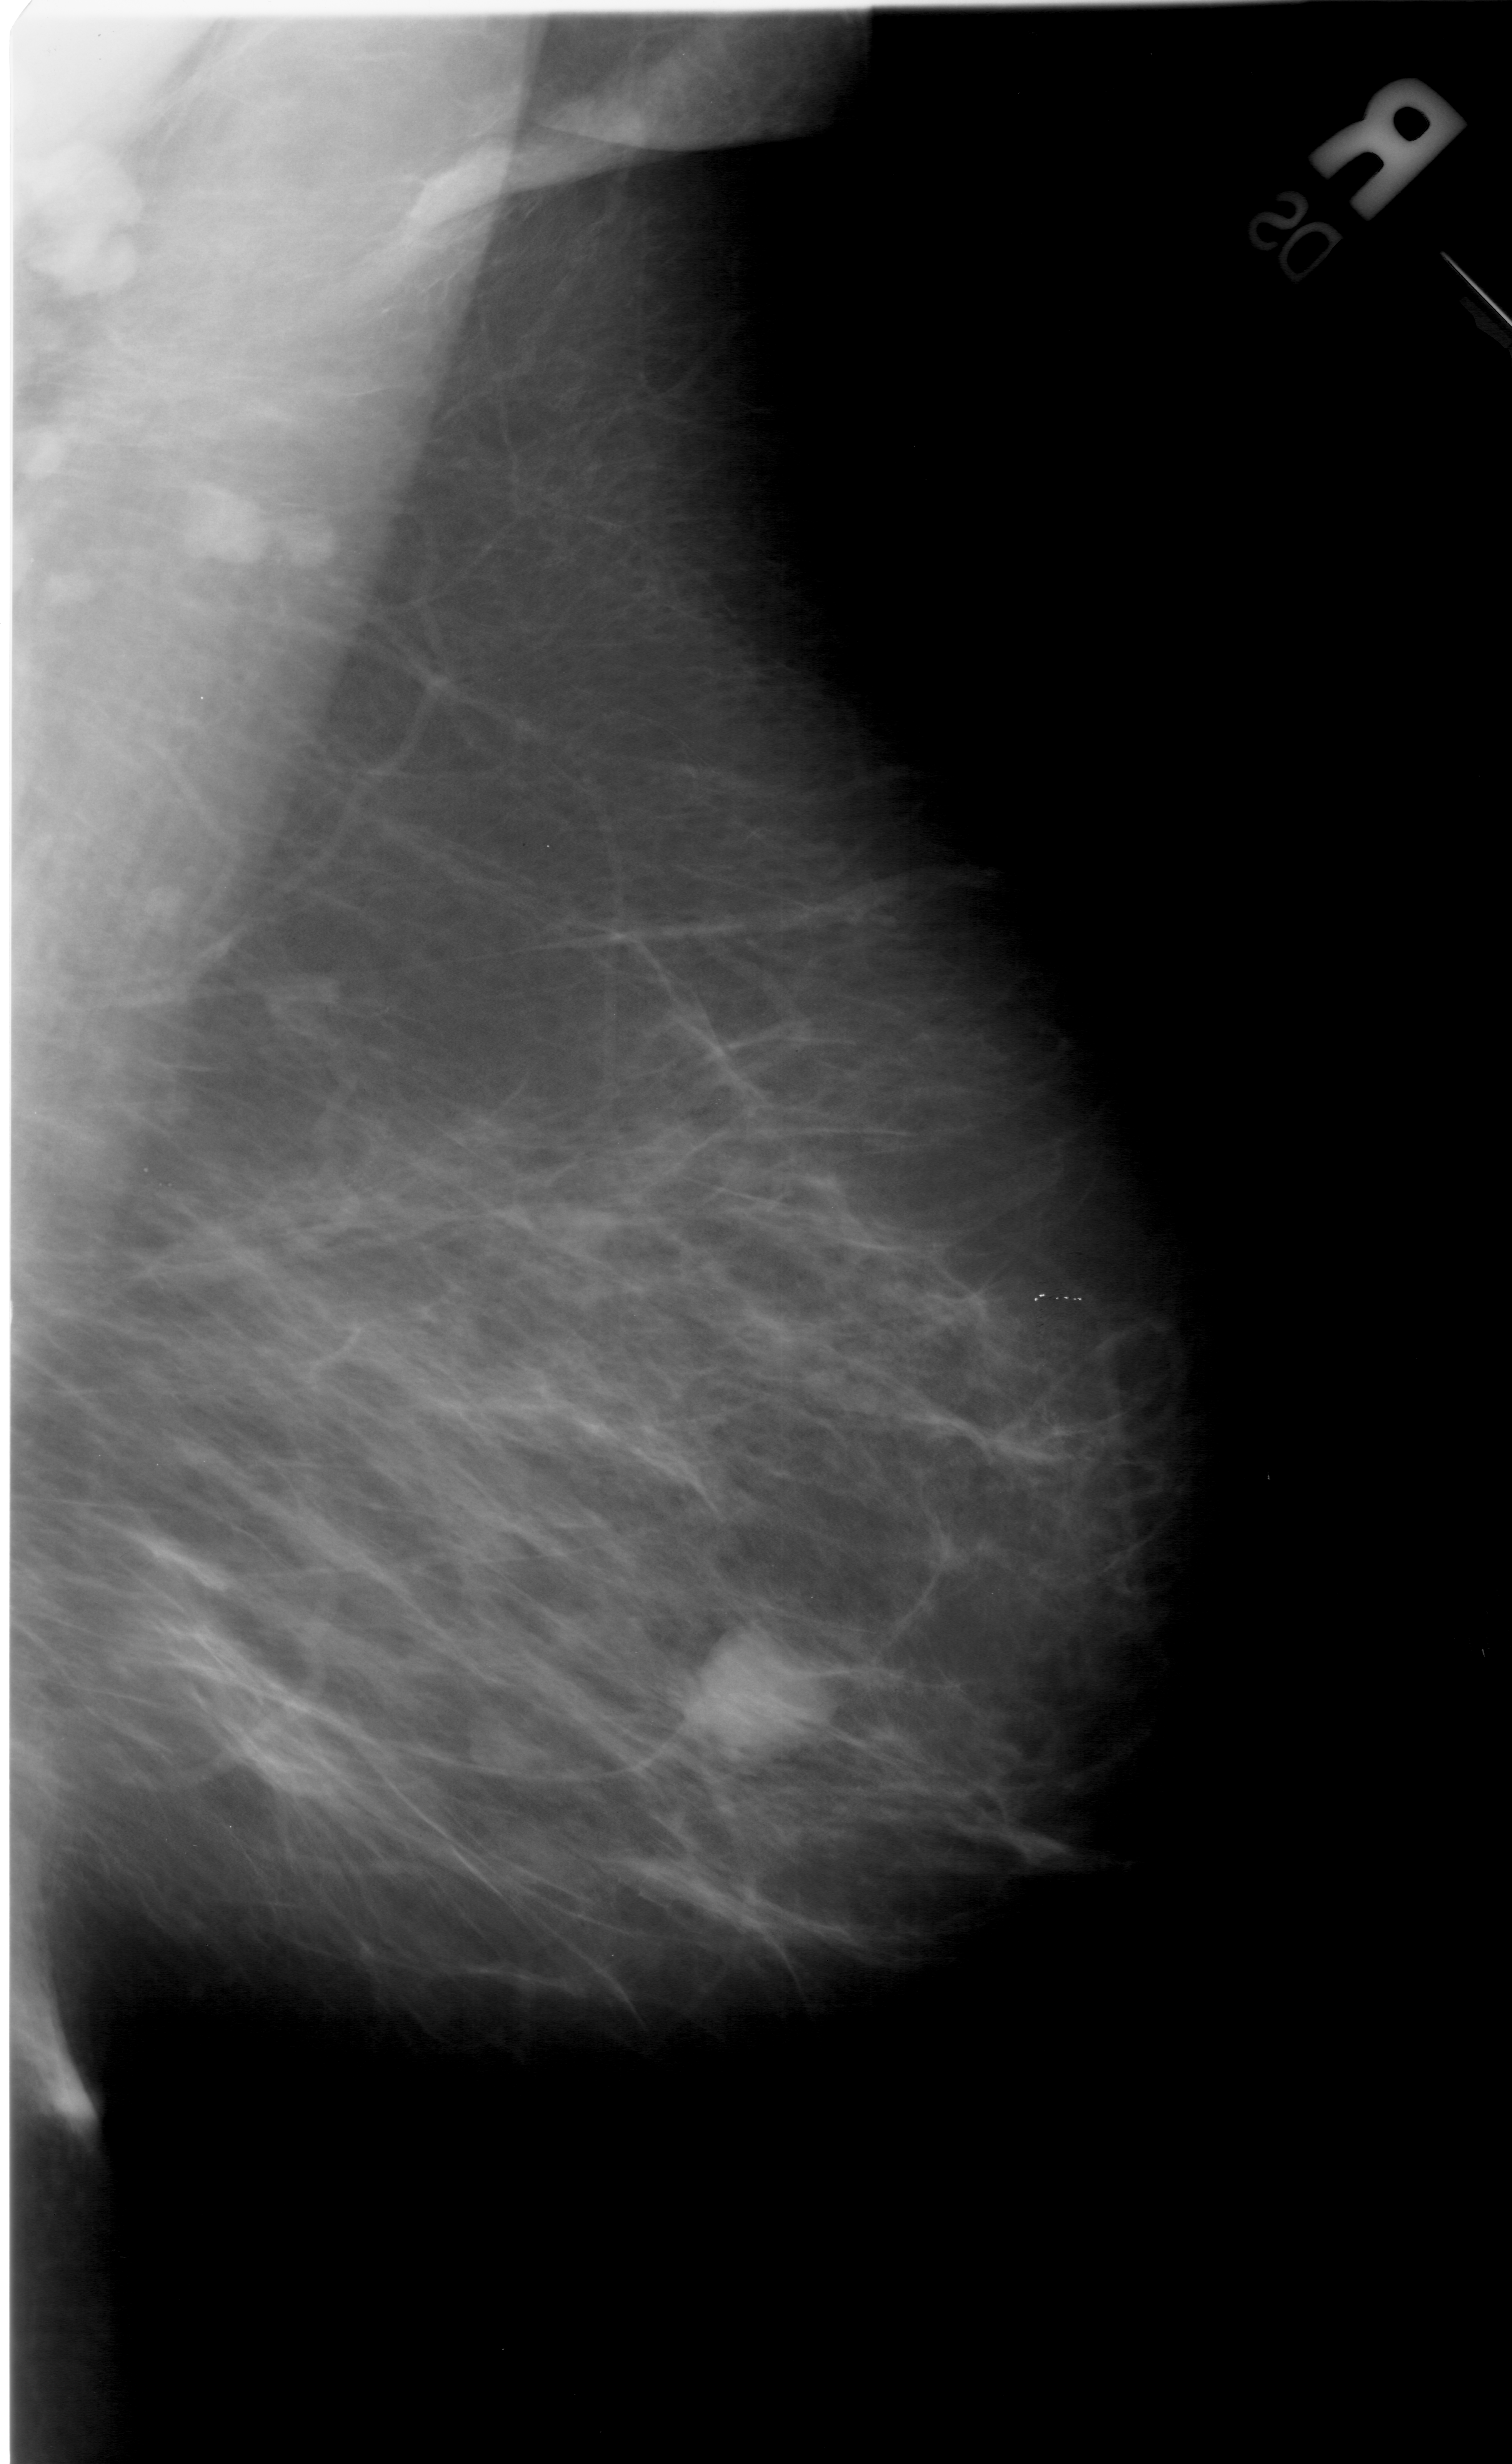
Scanned film-screen mammogram; right breast; mediolateral oblique (MLO) view; breast composition: heterogeneously dense (BI-RADS density category 3 of 4).
- Finding: mass, shape lobulated, margins circumscribed; BI-RADS assessment category 4; pathology (as recorded): benign.